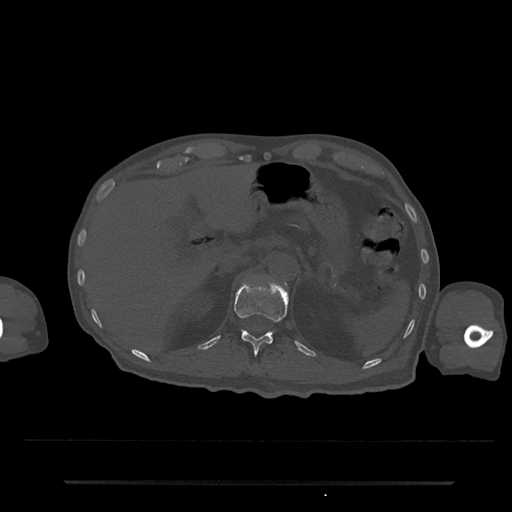
CT including the spine, one axial slice; position 187 of 797 along the scan axis; 120 kVp; bone window (W 1800 / L 400 HU); 512 × 512 image matrix, field of view 427 × 427 mm. Patient: male, 74 years. Case-level facts recorded for this patient, not image findings: primary cancer: prostate.
Outlined on this slice (semi-automatically segmented with operator editing):
- T12 vertebra: bounding box <234,283,289,356> (left, top, right, bottom; pixels)